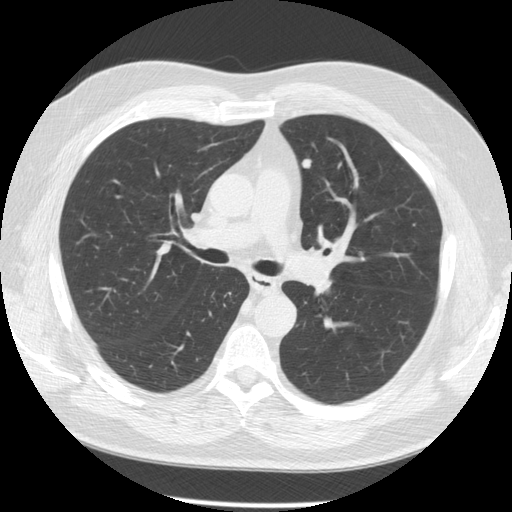
Low-dose screening chest CT, one axial slice; slice 86 of 137 in the series (ordered by position); 120 kVp; lung window (W 1500 / L -600 HU); 2.5 mm slice thickness; 512 × 512 image matrix, field of view 370 × 370 mm.
Outlined on this slice (outlined manually by an expert reader):
- lesion 1 (tumor, upper lobe of left lung): bounding box <302,159,312,169> (left, top, right, bottom; pixels)